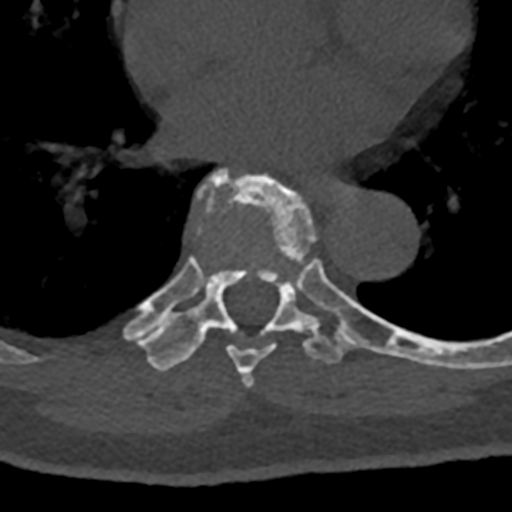
CT including the spine, one axial slice; slice 733 of 797 in the series (ordered by position); reconstruction kernel Br40s/3; 120 kVp; bone window (W 1800 / L 400 HU); 0.5 mm slice thickness; 512 × 512 image matrix, field of view 160 × 160 mm. Male patient, age 74 years. From the clinical record (not read from this slice): primary cancer: renal; vertebrae with lytic lesions (as recorded): T10, L1, L2, L3, L4, L5.
Outlined on this slice (semi-automatic segmentation, software-assisted and operator-edited):
- T7 vertebra: bounding box <198,169,355,386> (left, top, right, bottom; pixels)
- T8 vertebra: <126,269,432,371>